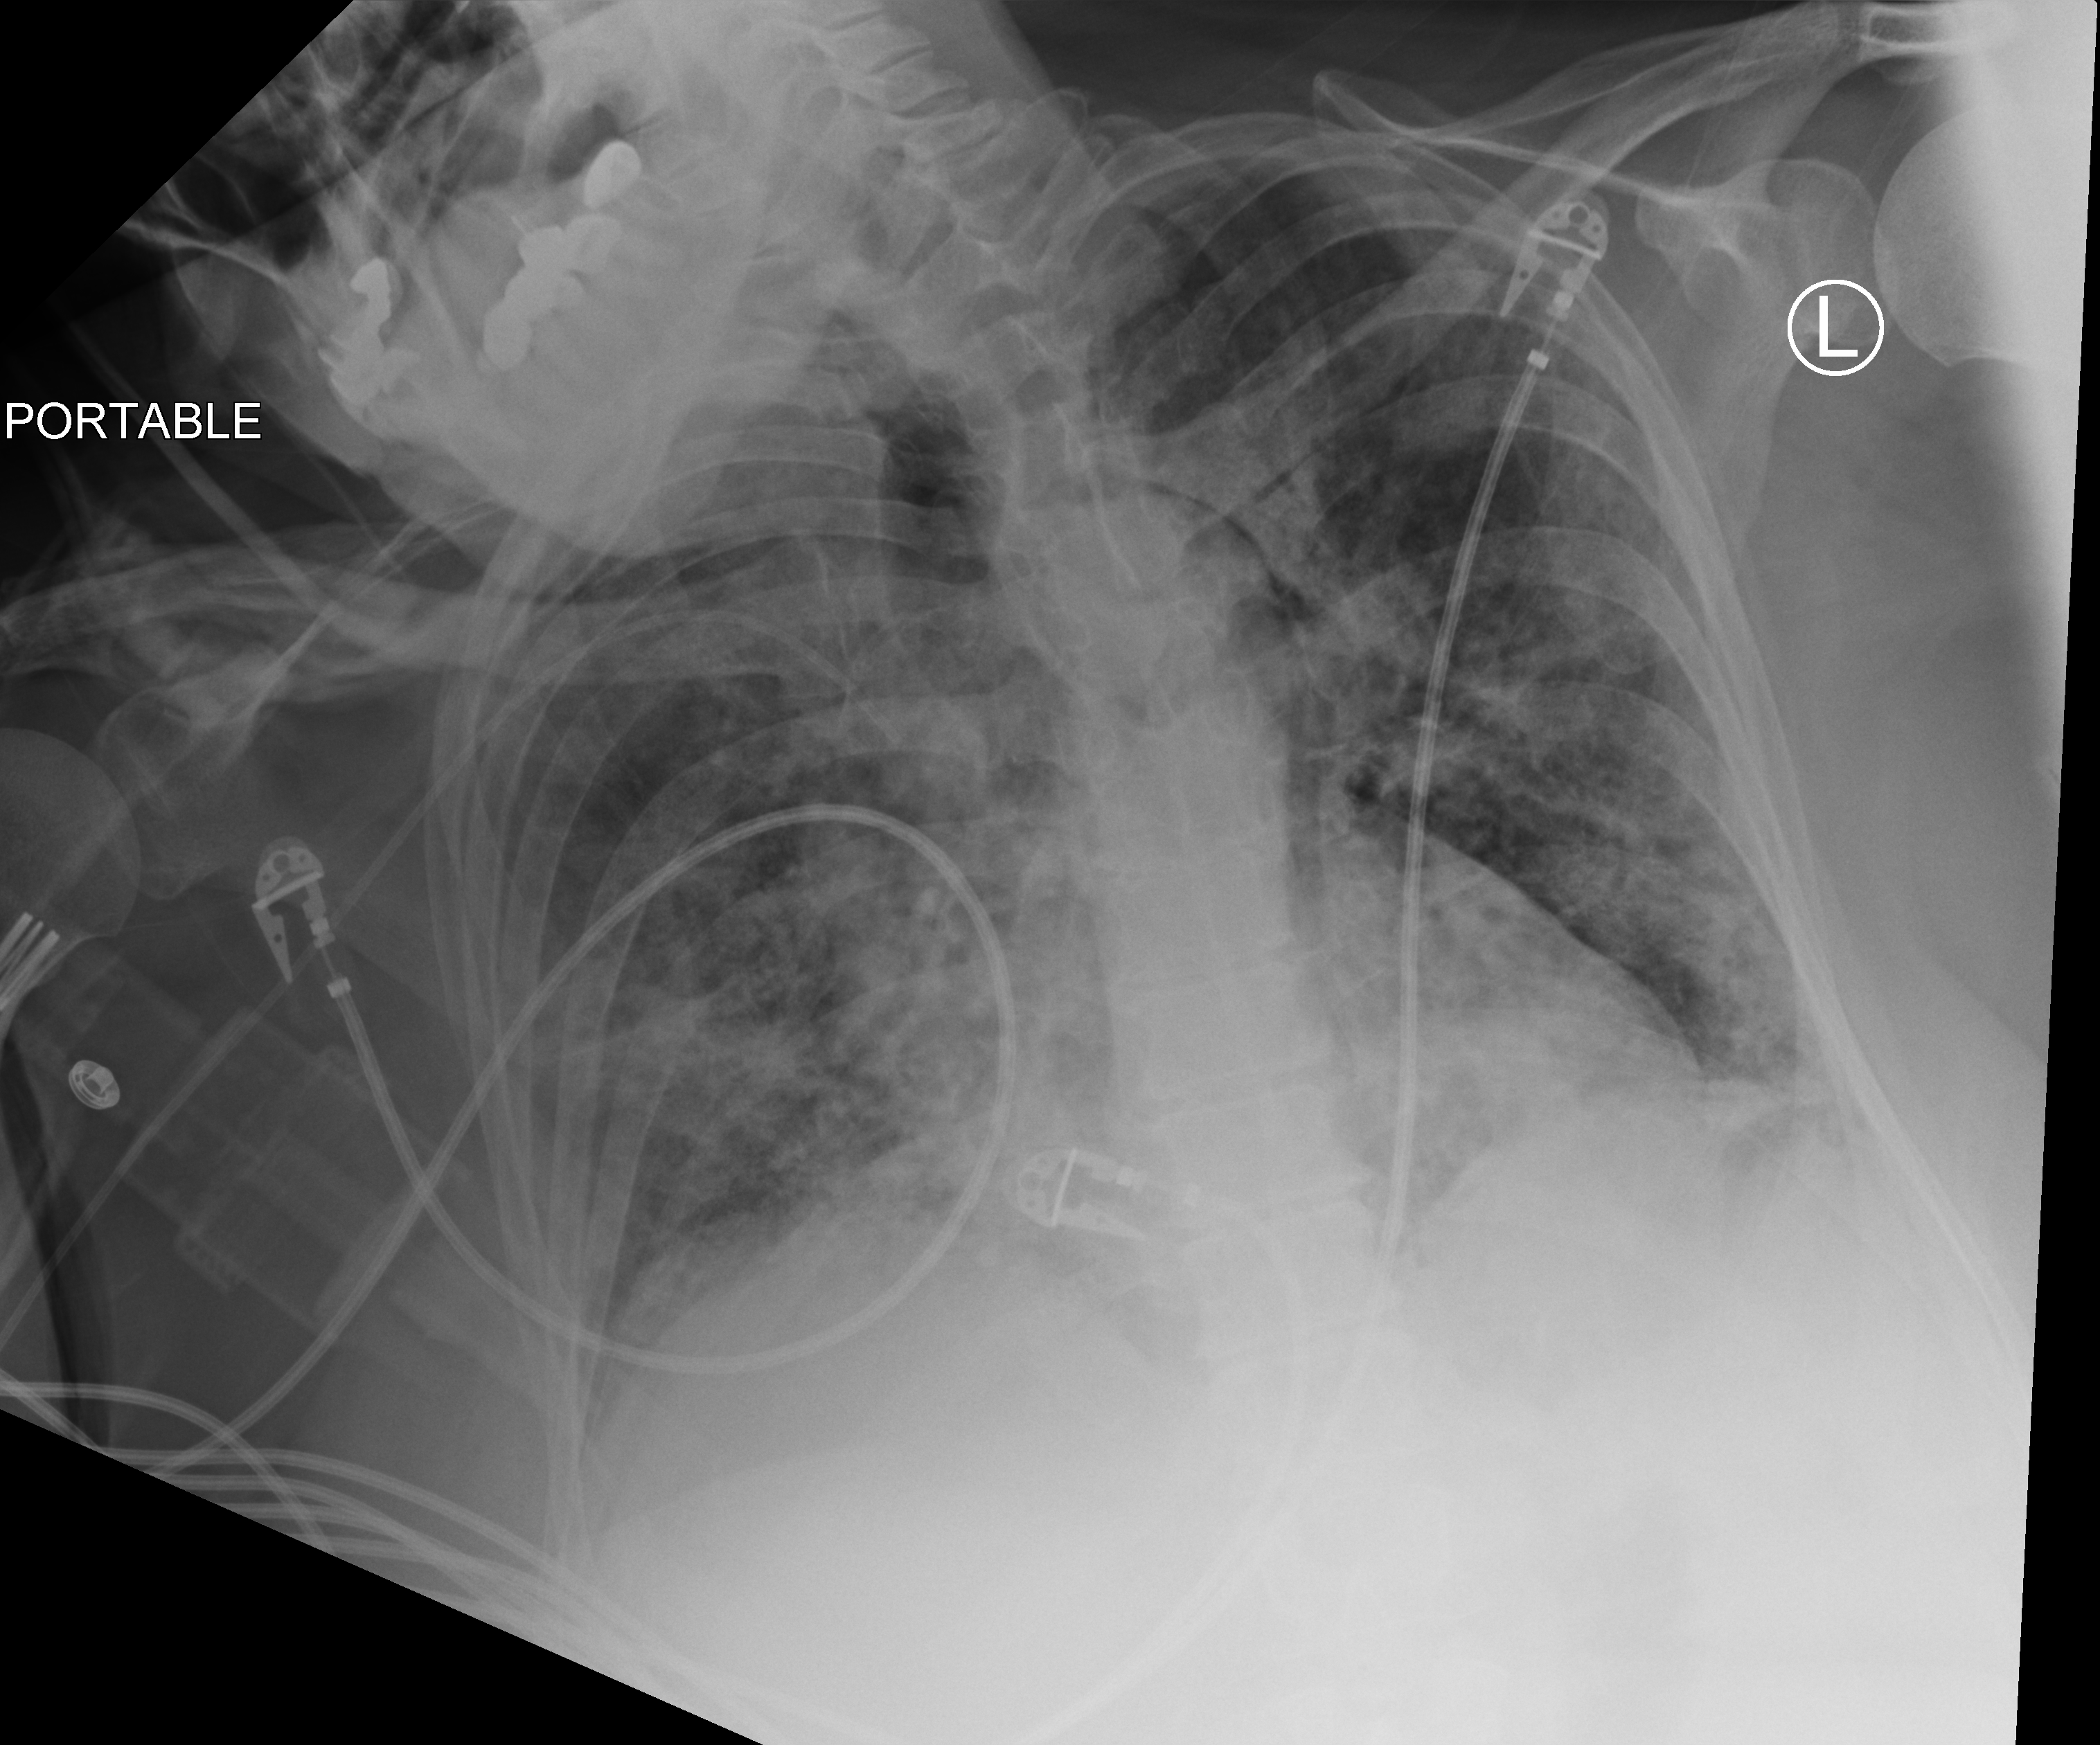
Chest X-ray (portable). Patient hospitalised with COVID-19; female, aged 60–74 years.
Admission-level facts for this patient (not findings on this image; timing relative to this image not recorded): chronic kidney disease (admission record): no.